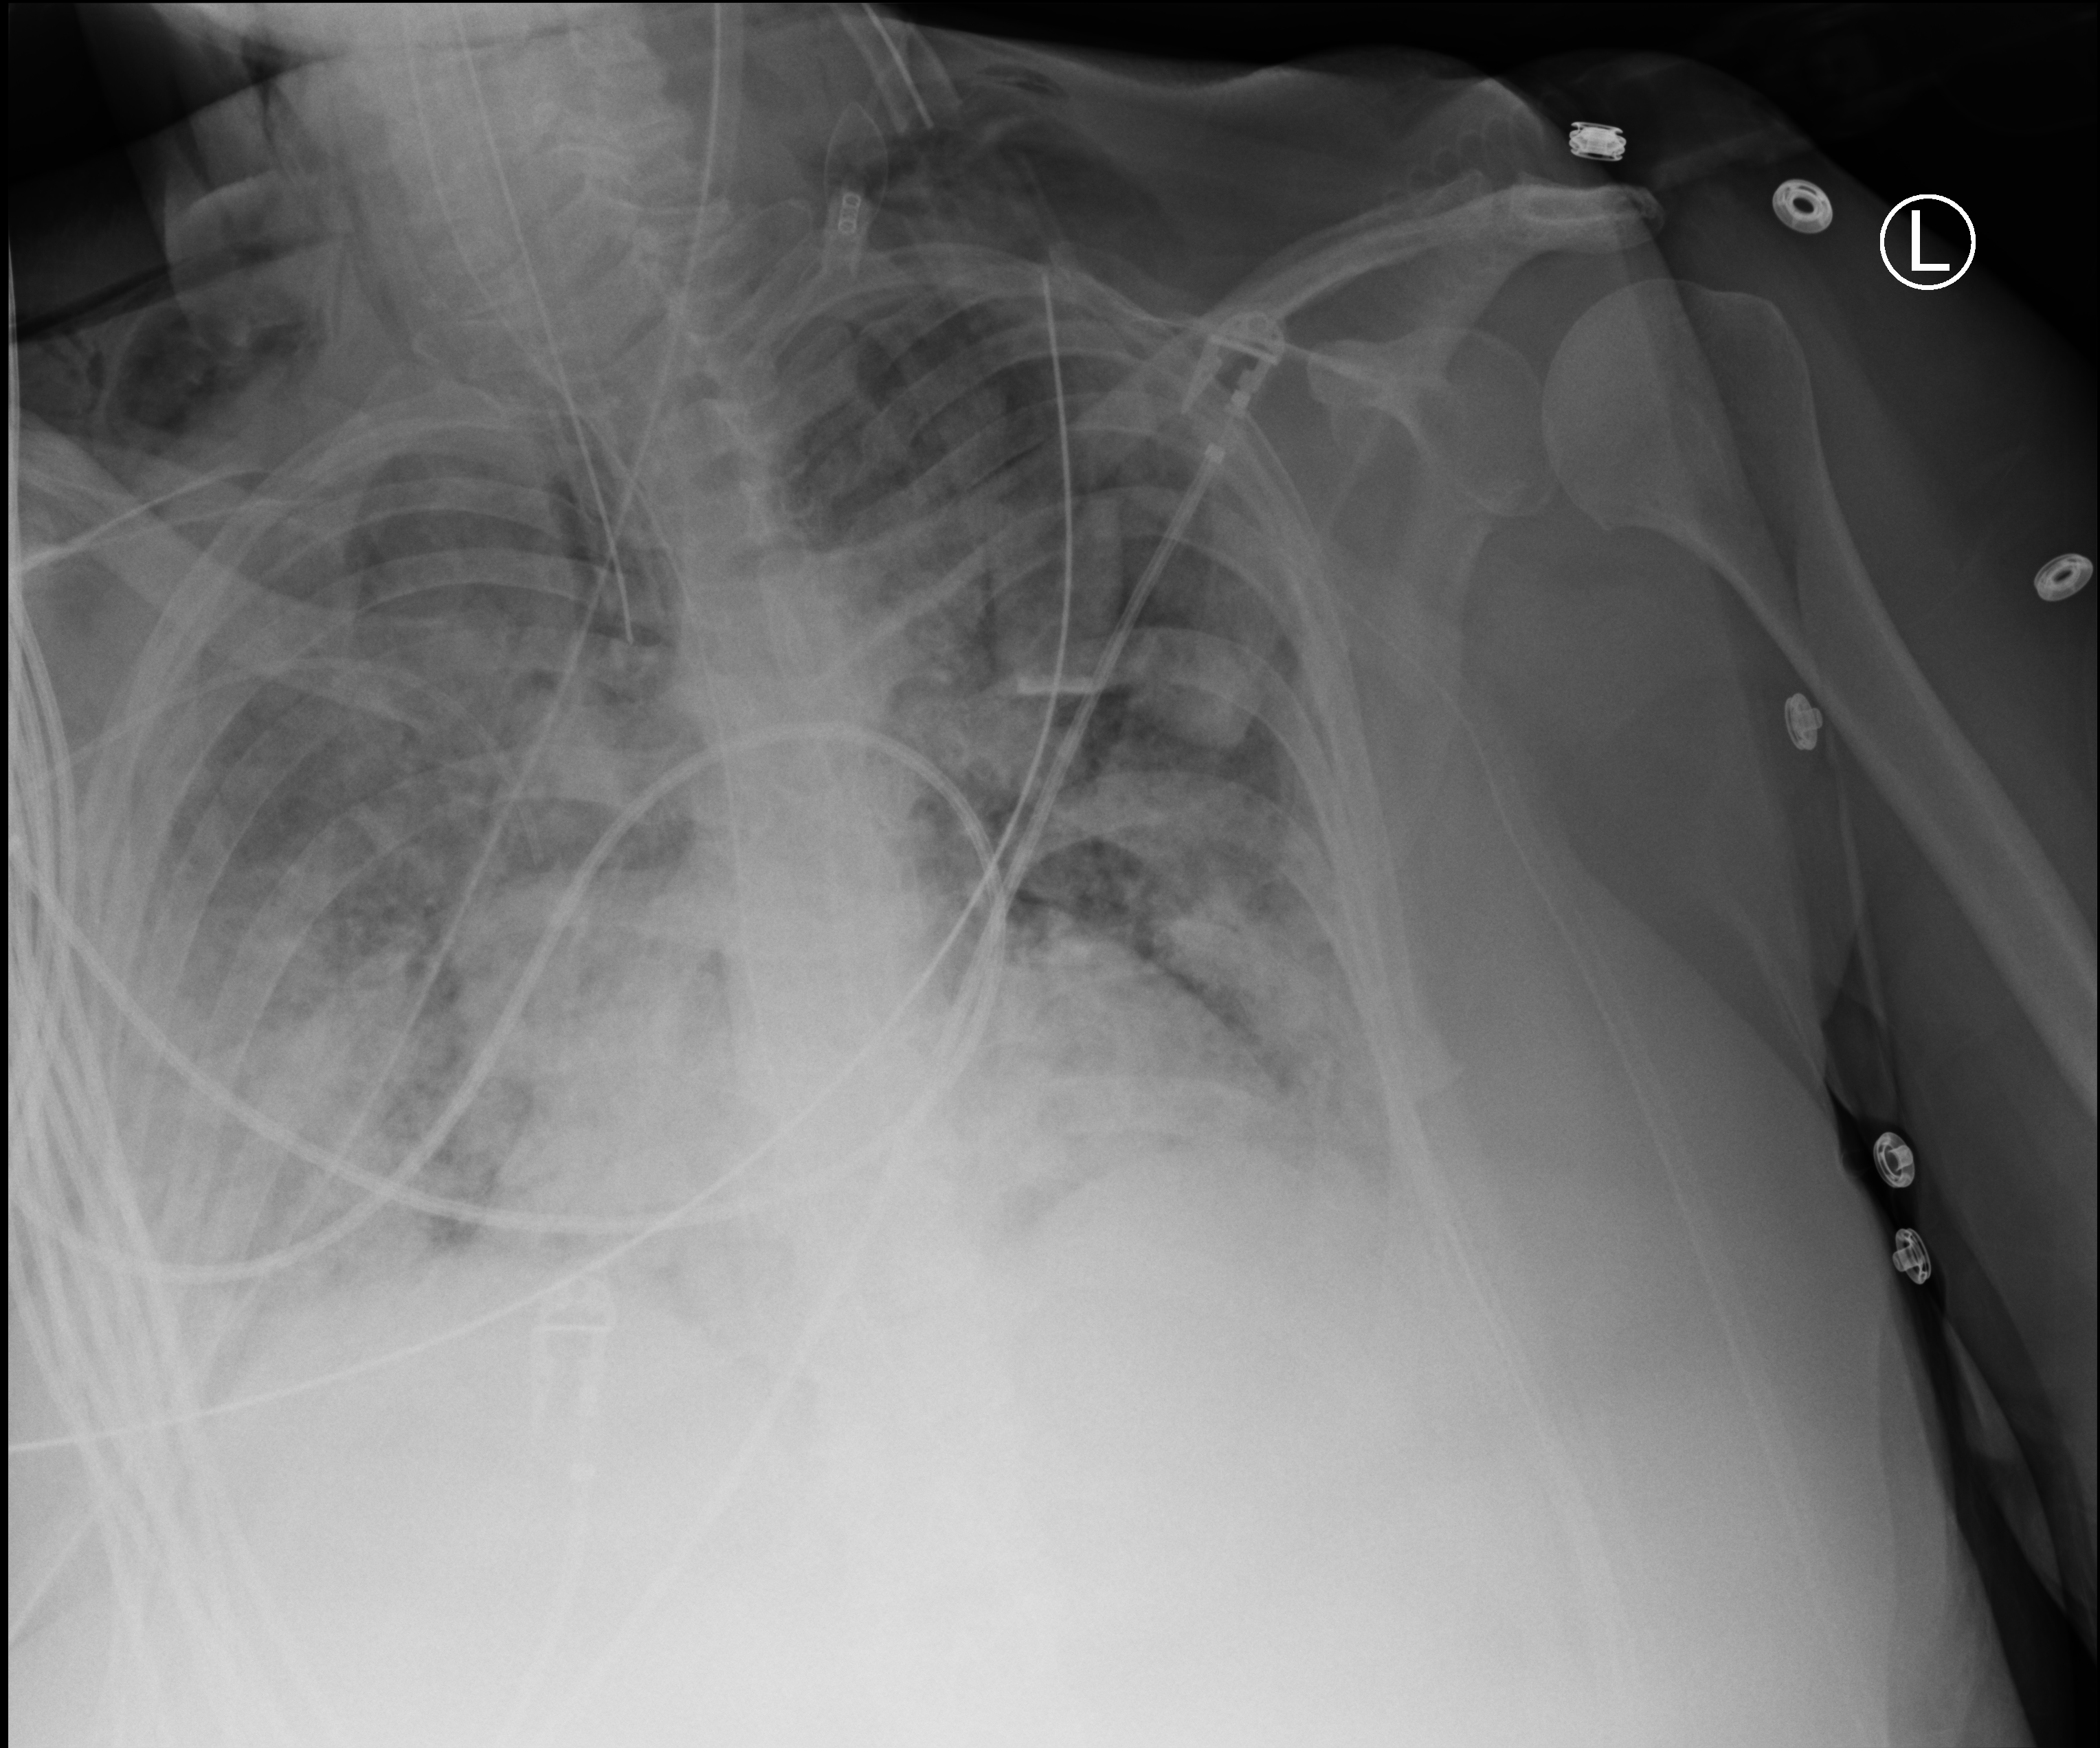
Portable chest radiograph; anteroposterior (AP) projection. Patient hospitalised with COVID-19; female, aged 60–74 years.
Admission-level facts for this patient (not findings on this image; timing relative to this image not recorded):
- length of hospital stay: 45 days
- admitted to intensive care during this hospital stay: yes
- smoking status (admission record): never